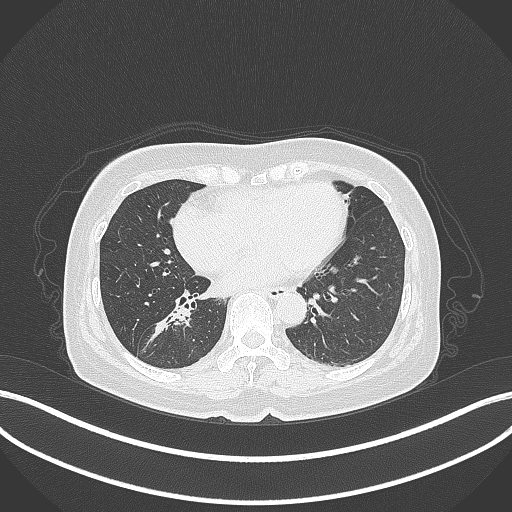
Chest CT, one axial slice. Slice 156 of 429 in the series (ordered by position). Reconstruction kernel B70f. Lung window (W 1500 / L -600 HU). 1 mm slice thickness. 512 × 512 image matrix, field of view 400 × 400 mm. Patient: female, 67 years. Case-level facts recorded for this patient, not image findings: clinical TNM (as recorded): T1c N1 M0.
Outlined on this slice (bounding box drawn by a radiologist):
- lung tumour (recorded histology: adenocarcinoma): bounding box (x1, y1, x2, y2) in pixels: (143, 302, 197, 353)